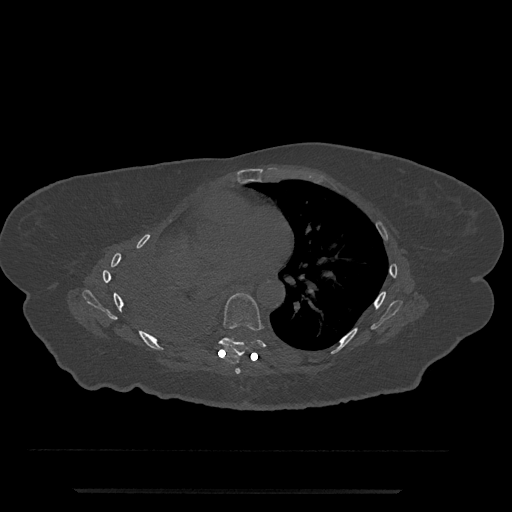
CT including the spine, one axial slice. Slice 439 of 797 in the series (ordered by position). Reconstruction kernel Br40s/3. 120 kVp. Bone window (W 1800 / L 400 HU). 0.5 mm slice thickness. 512 × 512 image matrix, field of view 440 × 440 mm. Patient: female, 51 years. From the clinical record (not read from this slice): primary cancer: neuro; vertebrae with lytic lesions (as recorded): T8.
Outlined on this slice (semi-automatic segmentation, software-assisted and operator-edited):
- T6 vertebra: bounding box [x1, y1, x2, y2] px = [235, 368, 241, 374]
- T7 vertebra: [219, 293, 277, 358]